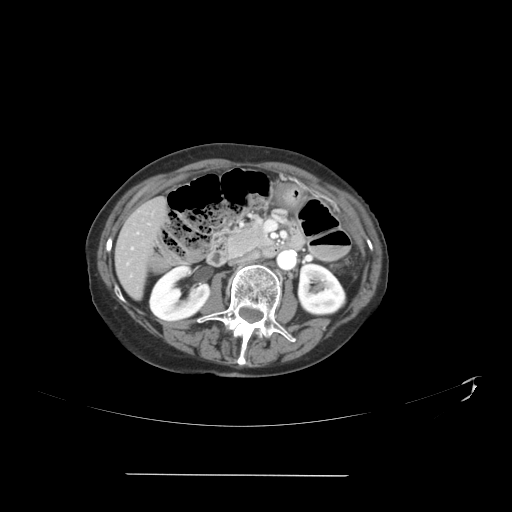
Contrast-enhanced abdominal CT, one axial slice; position 14 of 41 along the scan axis; reconstruction kernel STANDARD; 120 kVp; intravenous contrast given; soft-tissue window (W 400 / L 40 HU); 512 × 512 image matrix, field of view 431 × 431 mm. Female patient, age 74 years. Case-level facts recorded for this patient, not image findings: diagnosis: colorectal cancer liver metastases, imaged before liver resection; multiple liver metastases: yes; largest metastasis: 3.3 cm; disease in both lobes: yes.
Outlined on this slice (manually delineated by an expert):
- hepatic veins: bounding box <127,232,139,265> (left, top, right, bottom; pixels)
- liver: <117,200,164,295>
- planned liver remnant (the part of the liver to remain after resection): <121,200,164,244>
- portal vein (with intrahepatic branches): <131,247,134,250>